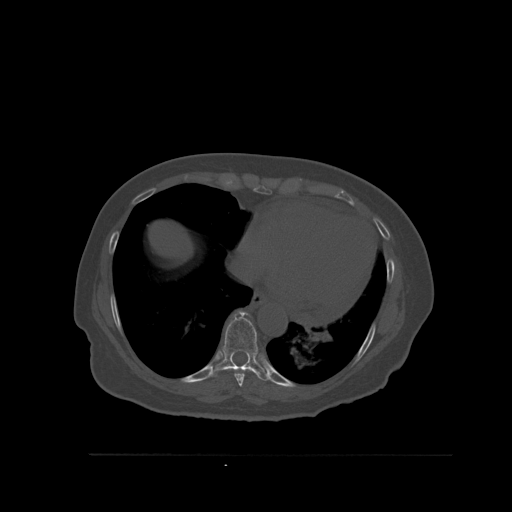
CT including the spine, one axial slice; position 339 of 527 along the scan axis; bone window (W 1800 / L 400 HU); 512 × 512 image matrix. Patient: female, 73 years. From the clinical record (not read from this slice): primary cancer: breast.
Annotated regions visible in this slice (semi-automatic segmentation, software-assisted and operator-edited):
- T8 vertebra: bounding box [x1, y1, x2, y2] px = [234, 369, 251, 387]
- T9 vertebra: [211, 310, 271, 381]